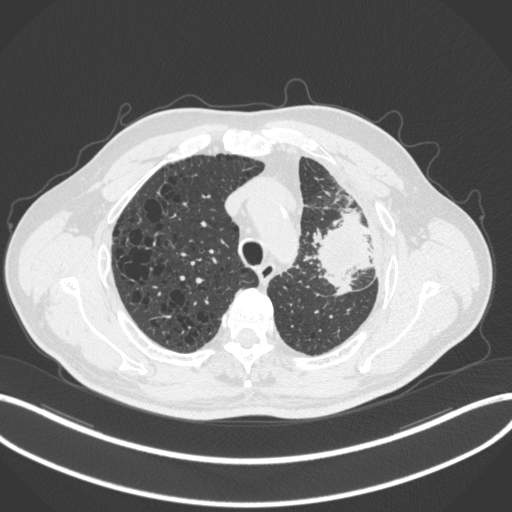
Chest CT, one axial slice. Position 236 of 286 along the scan axis. Reconstruction kernel B31f. Lung window (W 1500 / L -600 HU). 1 mm slice thickness. 512 × 512 image matrix, field of view 400 × 400 mm. Patient: male, 68 years. Case-level facts recorded for this patient, not image findings: clinical TNM (as recorded): T3 N3 M1.
Annotated regions visible in this slice (bounding box drawn by a radiologist):
- lung tumour (recorded histology: adenocarcinoma): bounding box (x1, y1, x2, y2) in pixels: (315, 203, 376, 298)